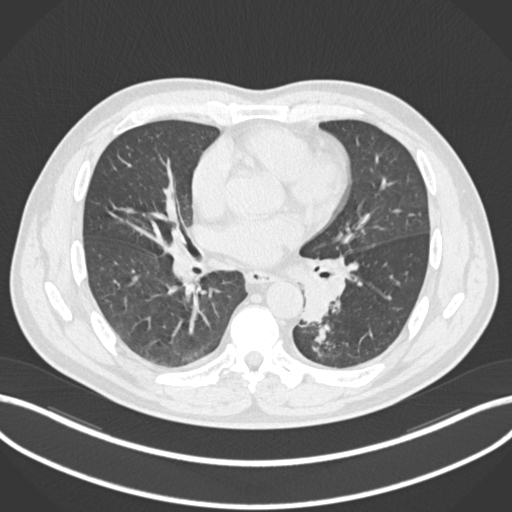
Chest CT, one axial slice. Position 109 of 223 along the scan axis. 120 kVp. Lung window (W 1500 / L -600 HU). 512 × 512 image matrix. Male patient, age 50 years. Case-level facts recorded for this patient, not image findings: clinical TNM (as recorded): T2a N3 M0.
Annotated regions visible in this slice (rectangle marked by the reading radiologist):
- lung tumour (recorded histology: squamous cell carcinoma): bounding box <293,264,351,326> (left, top, right, bottom; pixels)